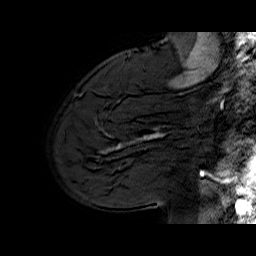
Breast MRI (dynamic contrast-enhanced), one sagittal slice; slice 48 of 70 in the series (ordered by position); dynamic contrast-enhanced series, time point 2 of 6 at this slice position (early post-contrast); 1.5 T; TE 6.5 ms, TR 33 ms; 256 × 256 image matrix, field of view 200 × 200 mm. Female patient. Case-level facts recorded for this patient, not image findings: setting: breast cancer imaged before/during neoadjuvant chemotherapy; receptor status: HER2-positive.
Annotated regions visible in this slice (semi-automatically segmented with operator editing):
- analysis volume of interest (the breast-tissue region the enhancement analysis was run in; not a lesion): bounding box (x1, y1, x2, y2) in pixels: (113, 112, 174, 170)
- tumour enhancement mask (voxels above the 100 % enhancement threshold inside the analysis volume of interest): (118, 133, 162, 147)